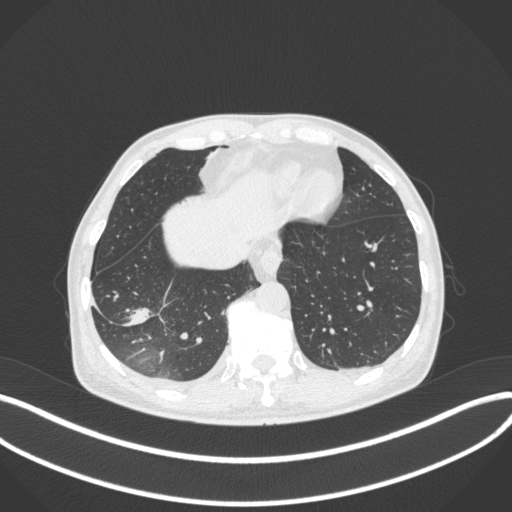
Chest CT, one axial slice; position 87 of 385 along the scan axis; reconstruction kernel B31f; 120 kVp; lung window (W 1500 / L -600 HU); 1 mm slice thickness; 512 × 512 image matrix. Male patient, age 64 years. From the clinical record (not read from this slice): clinical TNM (as recorded): T3 N0 M0.
Structures marked on this image (rectangle marked by the reading radiologist):
- lung tumour (recorded histology: adenocarcinoma): box from (x=121, y=303) to (x=161, y=333) px